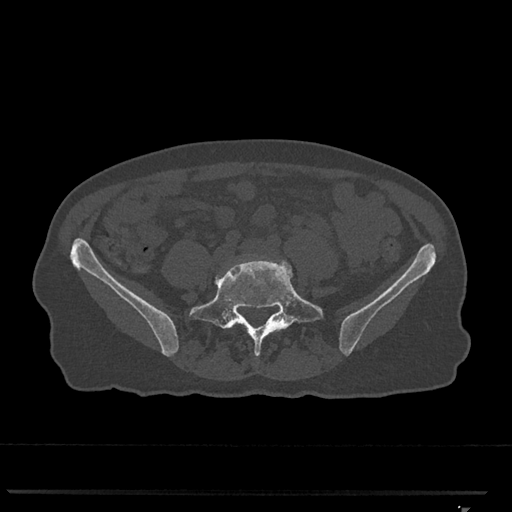
CT including the spine, one axial slice; slice 160 of 793 in the series (ordered by position); reconstruction kernel Br40s/3; bone window (W 1800 / L 400 HU); 0.5 mm slice thickness; 512 × 512 image matrix, field of view 380 × 380 mm. Patient: female, 62 years. From the clinical record (not read from this slice): primary cancer: renal.
Annotated regions visible in this slice (semi-automatically segmented with operator editing):
- L4 vertebra: bounding box <217,258,257,279> (left, top, right, bottom; pixels)
- L5 vertebra: <189,259,323,356>